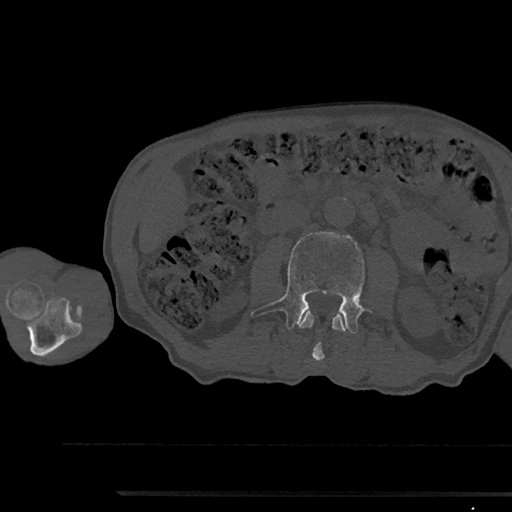
CT including the spine, one axial slice. Position 513 of 797 along the scan axis. Reconstruction kernel Br40s/3. Bone window (W 1800 / L 400 HU). 0.5 mm slice thickness. 512 × 512 image matrix. Patient: male, 79 years. From the clinical record (not read from this slice): primary cancer: prostate.
Outlined on this slice (semi-automatic segmentation, software-assisted and operator-edited):
- L2 vertebra: bounding box <298,311,347,362> (left, top, right, bottom; pixels)
- L3 vertebra: <251,232,374,333>